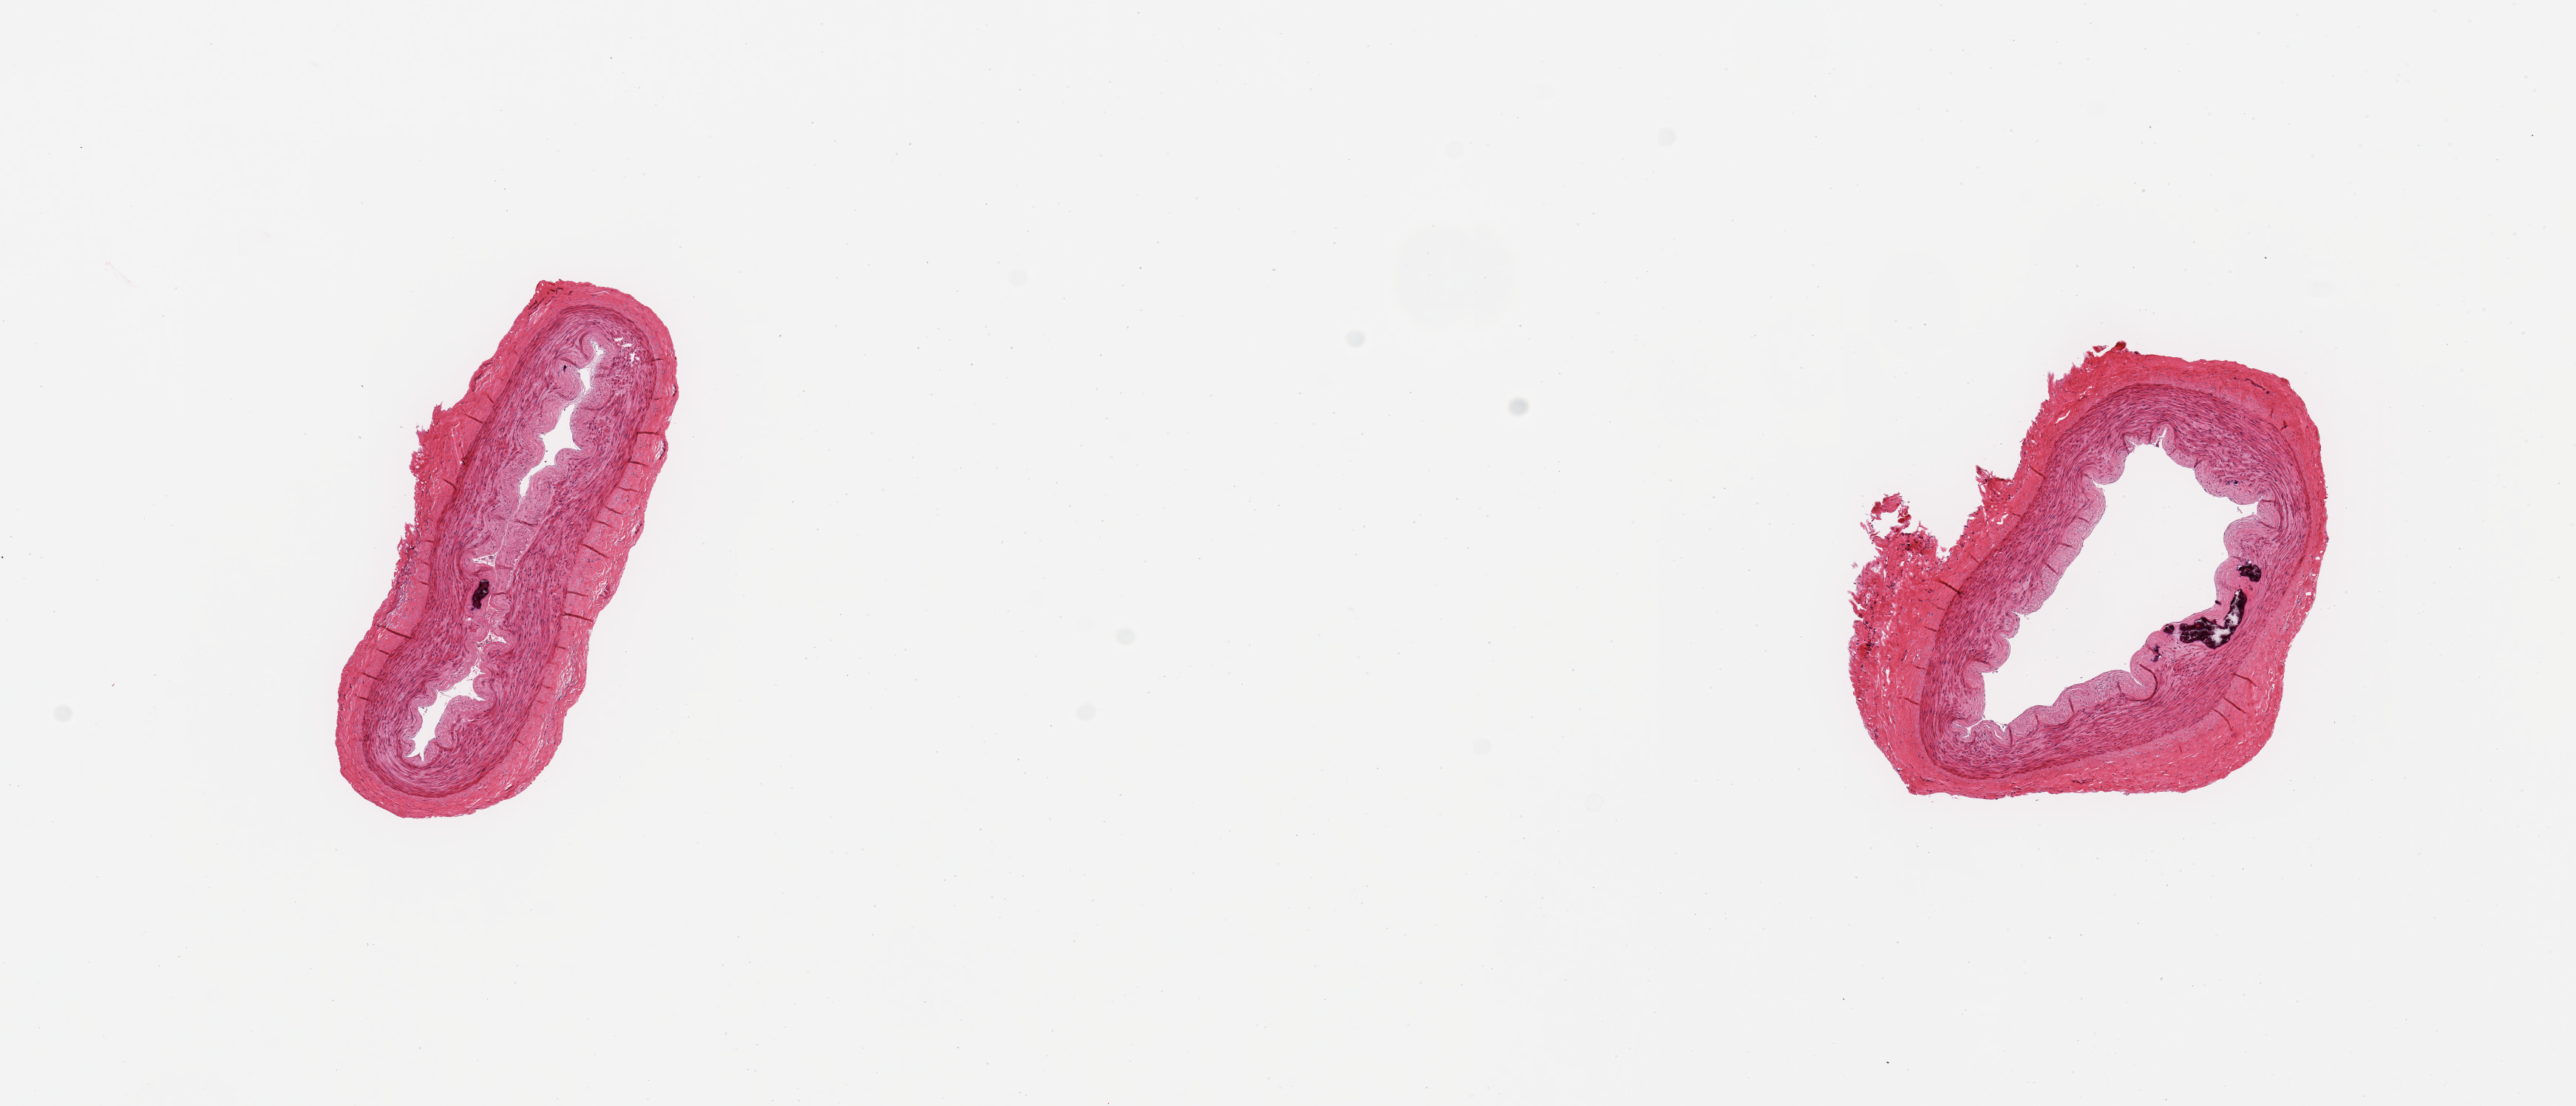
Digitized H&E-stained section — whole scanned area (about 13.8 x 5.9 mm) shown as a low-resolution overview, PAXgene-fixed paraffin-embedded (PFPE) section, sampled site (target tissue): tibial artery, tissue donor sample. Donor sex: male.
Pathologist's review note for this sample: 2 pieces; mild atherosclerosis with focal calcification.